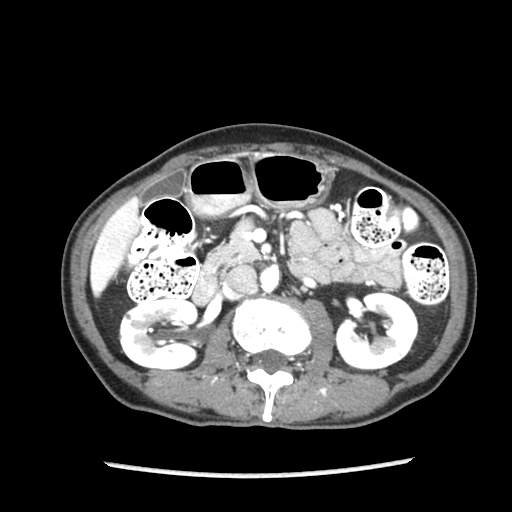
Contrast-enhanced abdominal CT (liver protocol), one axial slice. Slice 38 of 87 in the series (ordered by position). Reconstruction kernel STANDARD. Soft-tissue window (W 400 / L 40 HU). 2.5 mm slice thickness. 512 × 512 image matrix, field of view 300 × 300 mm. Case-level facts recorded for this patient, not image findings: diagnosis: hepatocellular carcinoma (patient treated with transarterial chemoembolisation; whether this scan precedes or follows treatment is not stated here); TNM stage (as recorded): Stage-IIIB; Child-Pugh class: A; tumour differentiation: well differentiated; tumour nodularity: uninodular.
Annotated regions visible in this slice (semi-automatically segmented with operator editing):
- liver parenchyma outside the tumour (the mass and vessels are separate outlines, so this box may not span the whole liver): bounding box [x1, y1, x2, y2] px = [90, 197, 140, 296]
- liver vessels: [97, 211, 127, 271]